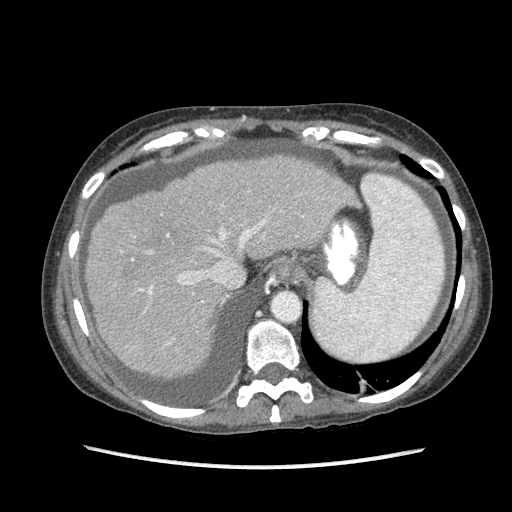
Contrast-enhanced abdominal CT (liver protocol), one axial slice. Slice 71 of 87 in the series (ordered by position). Reconstruction kernel STANDARD. Soft-tissue window (W 400 / L 40 HU). 512 × 512 image matrix, field of view 340 × 340 mm. Case-level facts recorded for this patient, not image findings: diagnosis: hepatocellular carcinoma (patient treated with transarterial chemoembolisation; whether this scan precedes or follows treatment is not stated here); TNM stage (as recorded): Stage-IIIB; Child-Pugh class: A; tumour differentiation: no biopsy; tumour nodularity: uninodular.
Outlined on this slice (semi-automatic segmentation, software-assisted and operator-edited):
- liver parenchyma outside the tumour (the mass and vessels are separate outlines, so this box may not span the whole liver): bounding box <85,154,356,376> (left, top, right, bottom; pixels)
- liver vessels: <131,204,267,345>